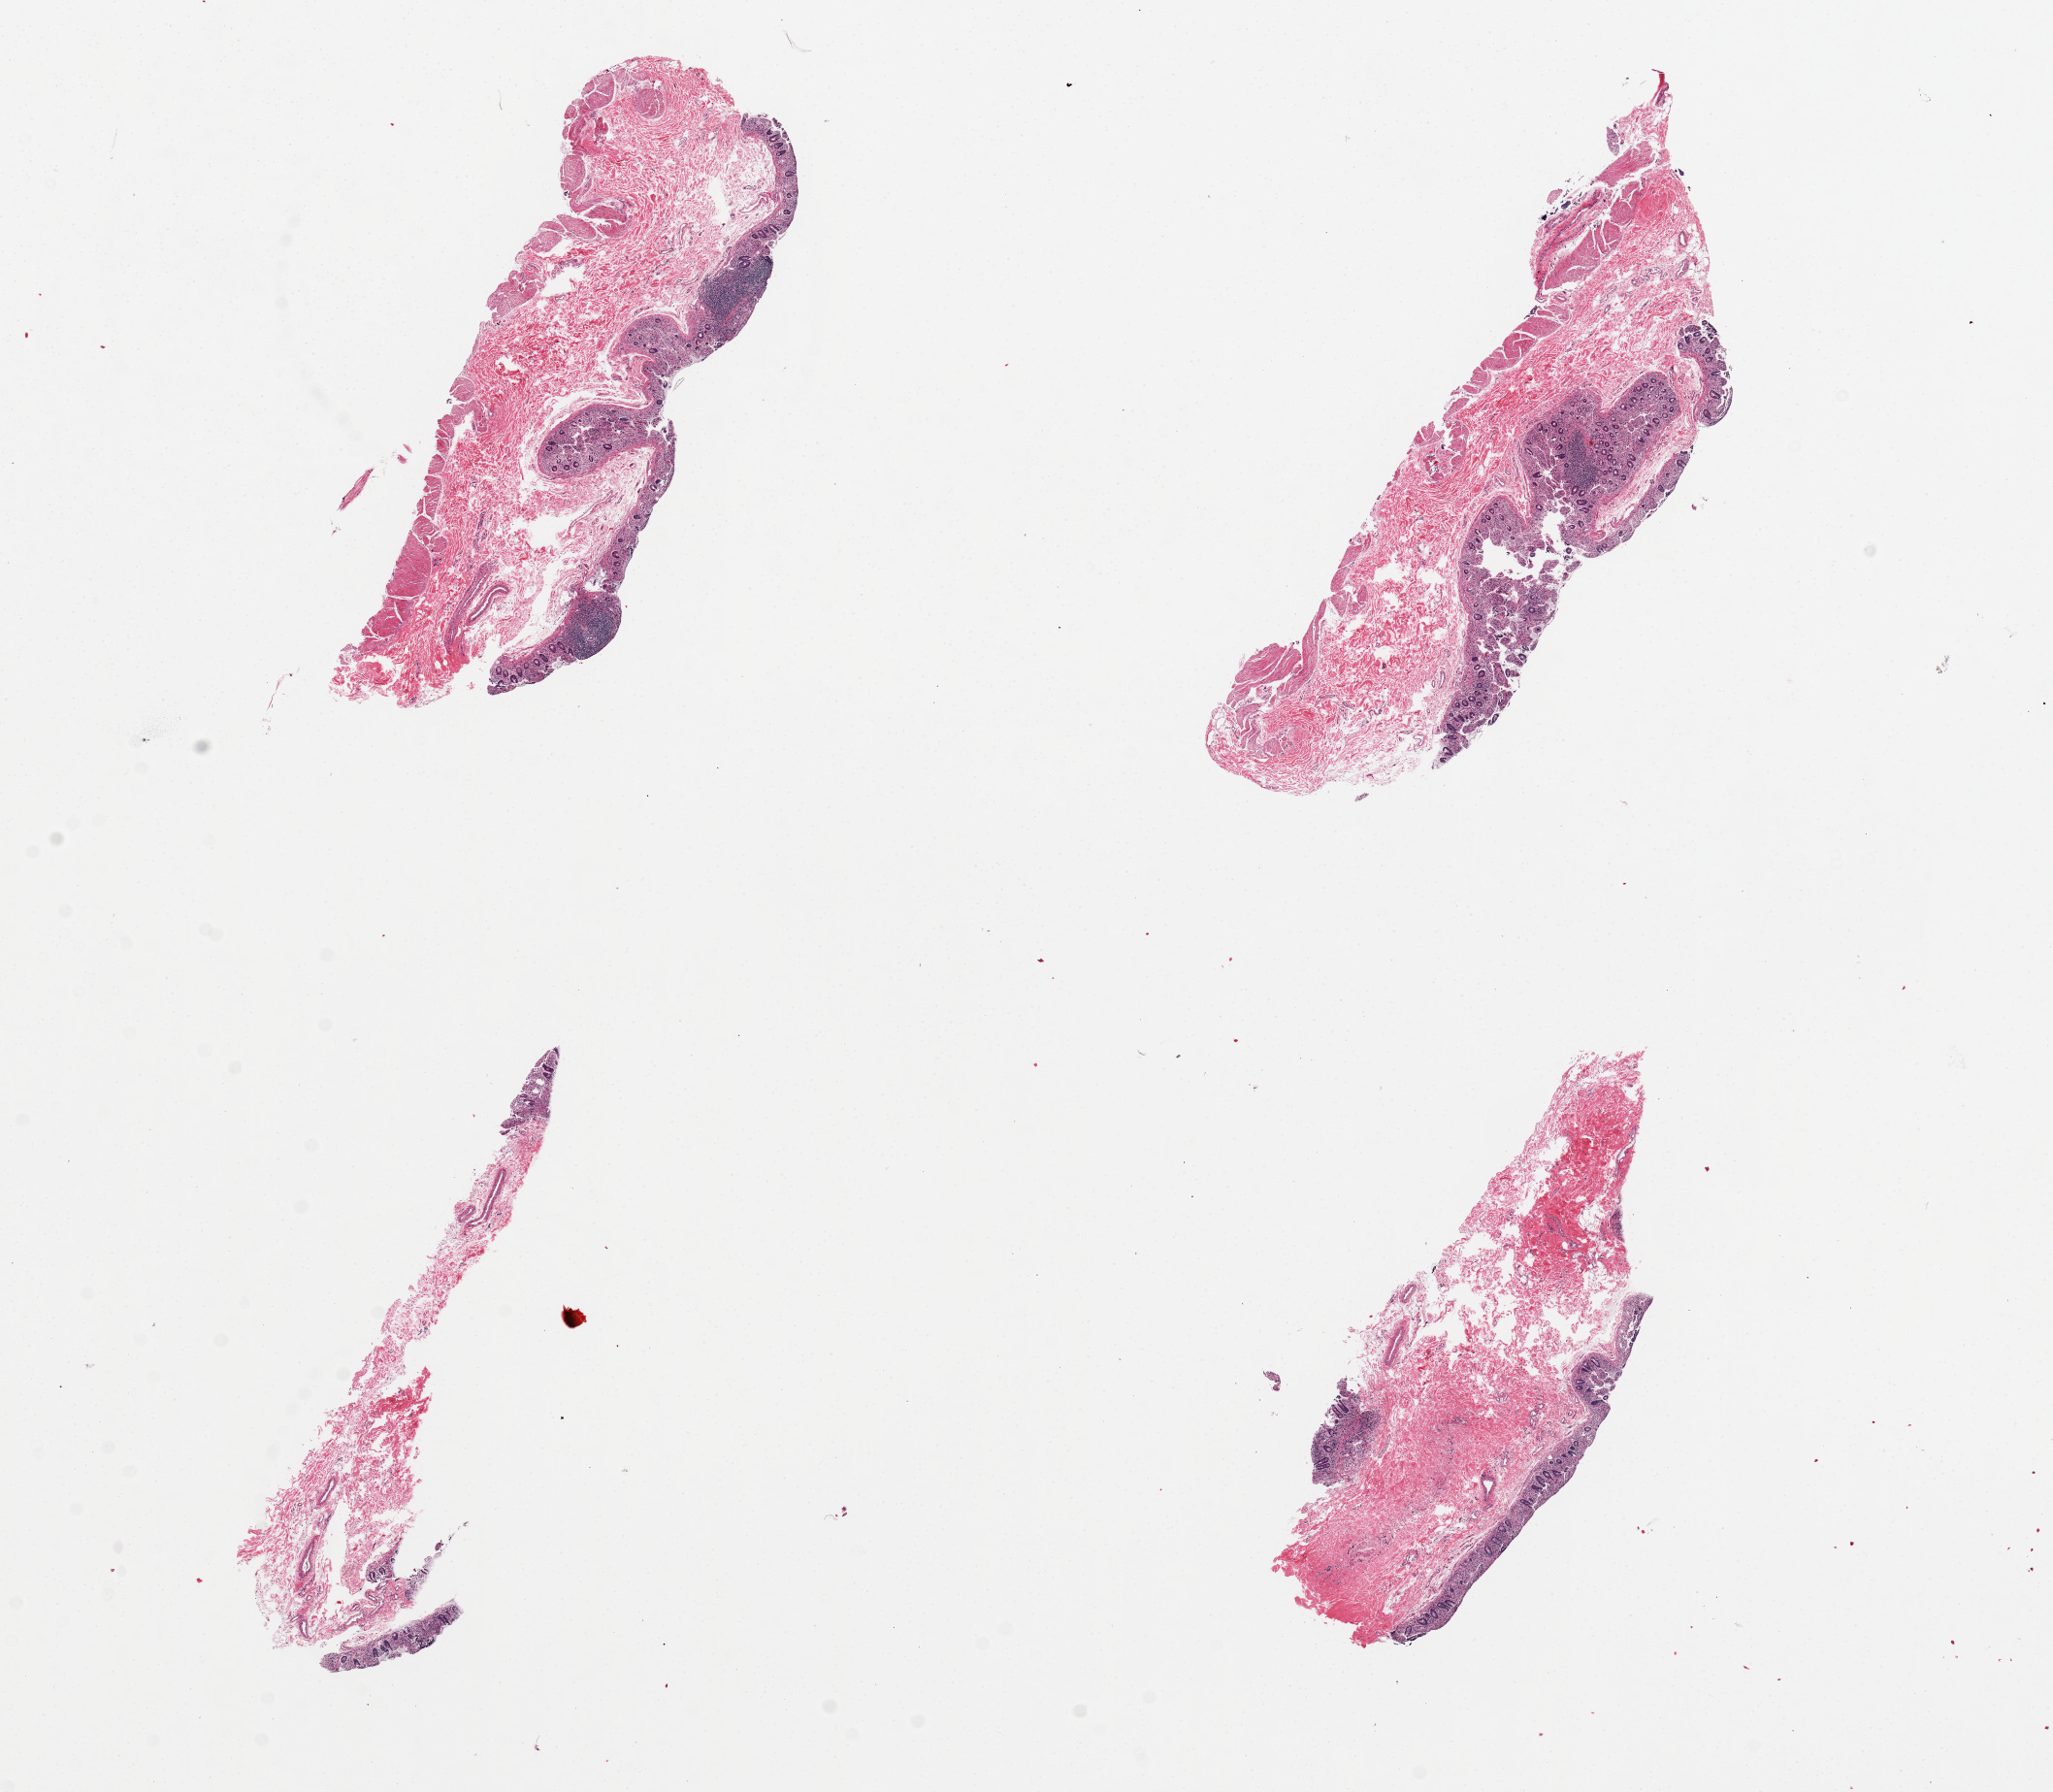
Haematoxylin and eosin whole-slide image — shown as a low-resolution overview of the whole scanned area (about 16.7 x 14.6 mm). PAXgene-fixed, paraffin-embedded tissue. Sampled site (target tissue): ileum. Tissue donor sample. Donor sex: male.
- pathologist's review note for this sample: 4 pieces; 3 small lymphoid nodules in 2 pieces